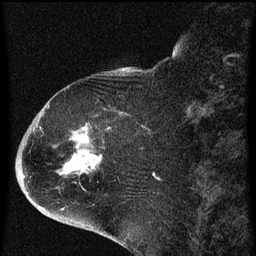
Breast MRI (dynamic contrast-enhanced), one sagittal slice. Position 22 of 60 along the scan axis. Dynamic contrast-enhanced series, image 2 of 4 at this slice position (ordered by acquisition). 1.5 T. TE 4.2 ms, TR 8 ms. 2 mm slice thickness. 256 × 256 image matrix, field of view 180 × 180 mm. Female patient, age 71 years.
Annotated regions visible in this slice (semi-automatically segmented with operator editing):
- analysis volume of interest (the breast-tissue region the enhancement analysis was run in; not a lesion): box from (x=32, y=86) to (x=140, y=205) px
- tumour enhancement mask (voxels above the 70 % enhancement threshold inside the analysis volume of interest): (x=64, y=128)–(x=109, y=169)